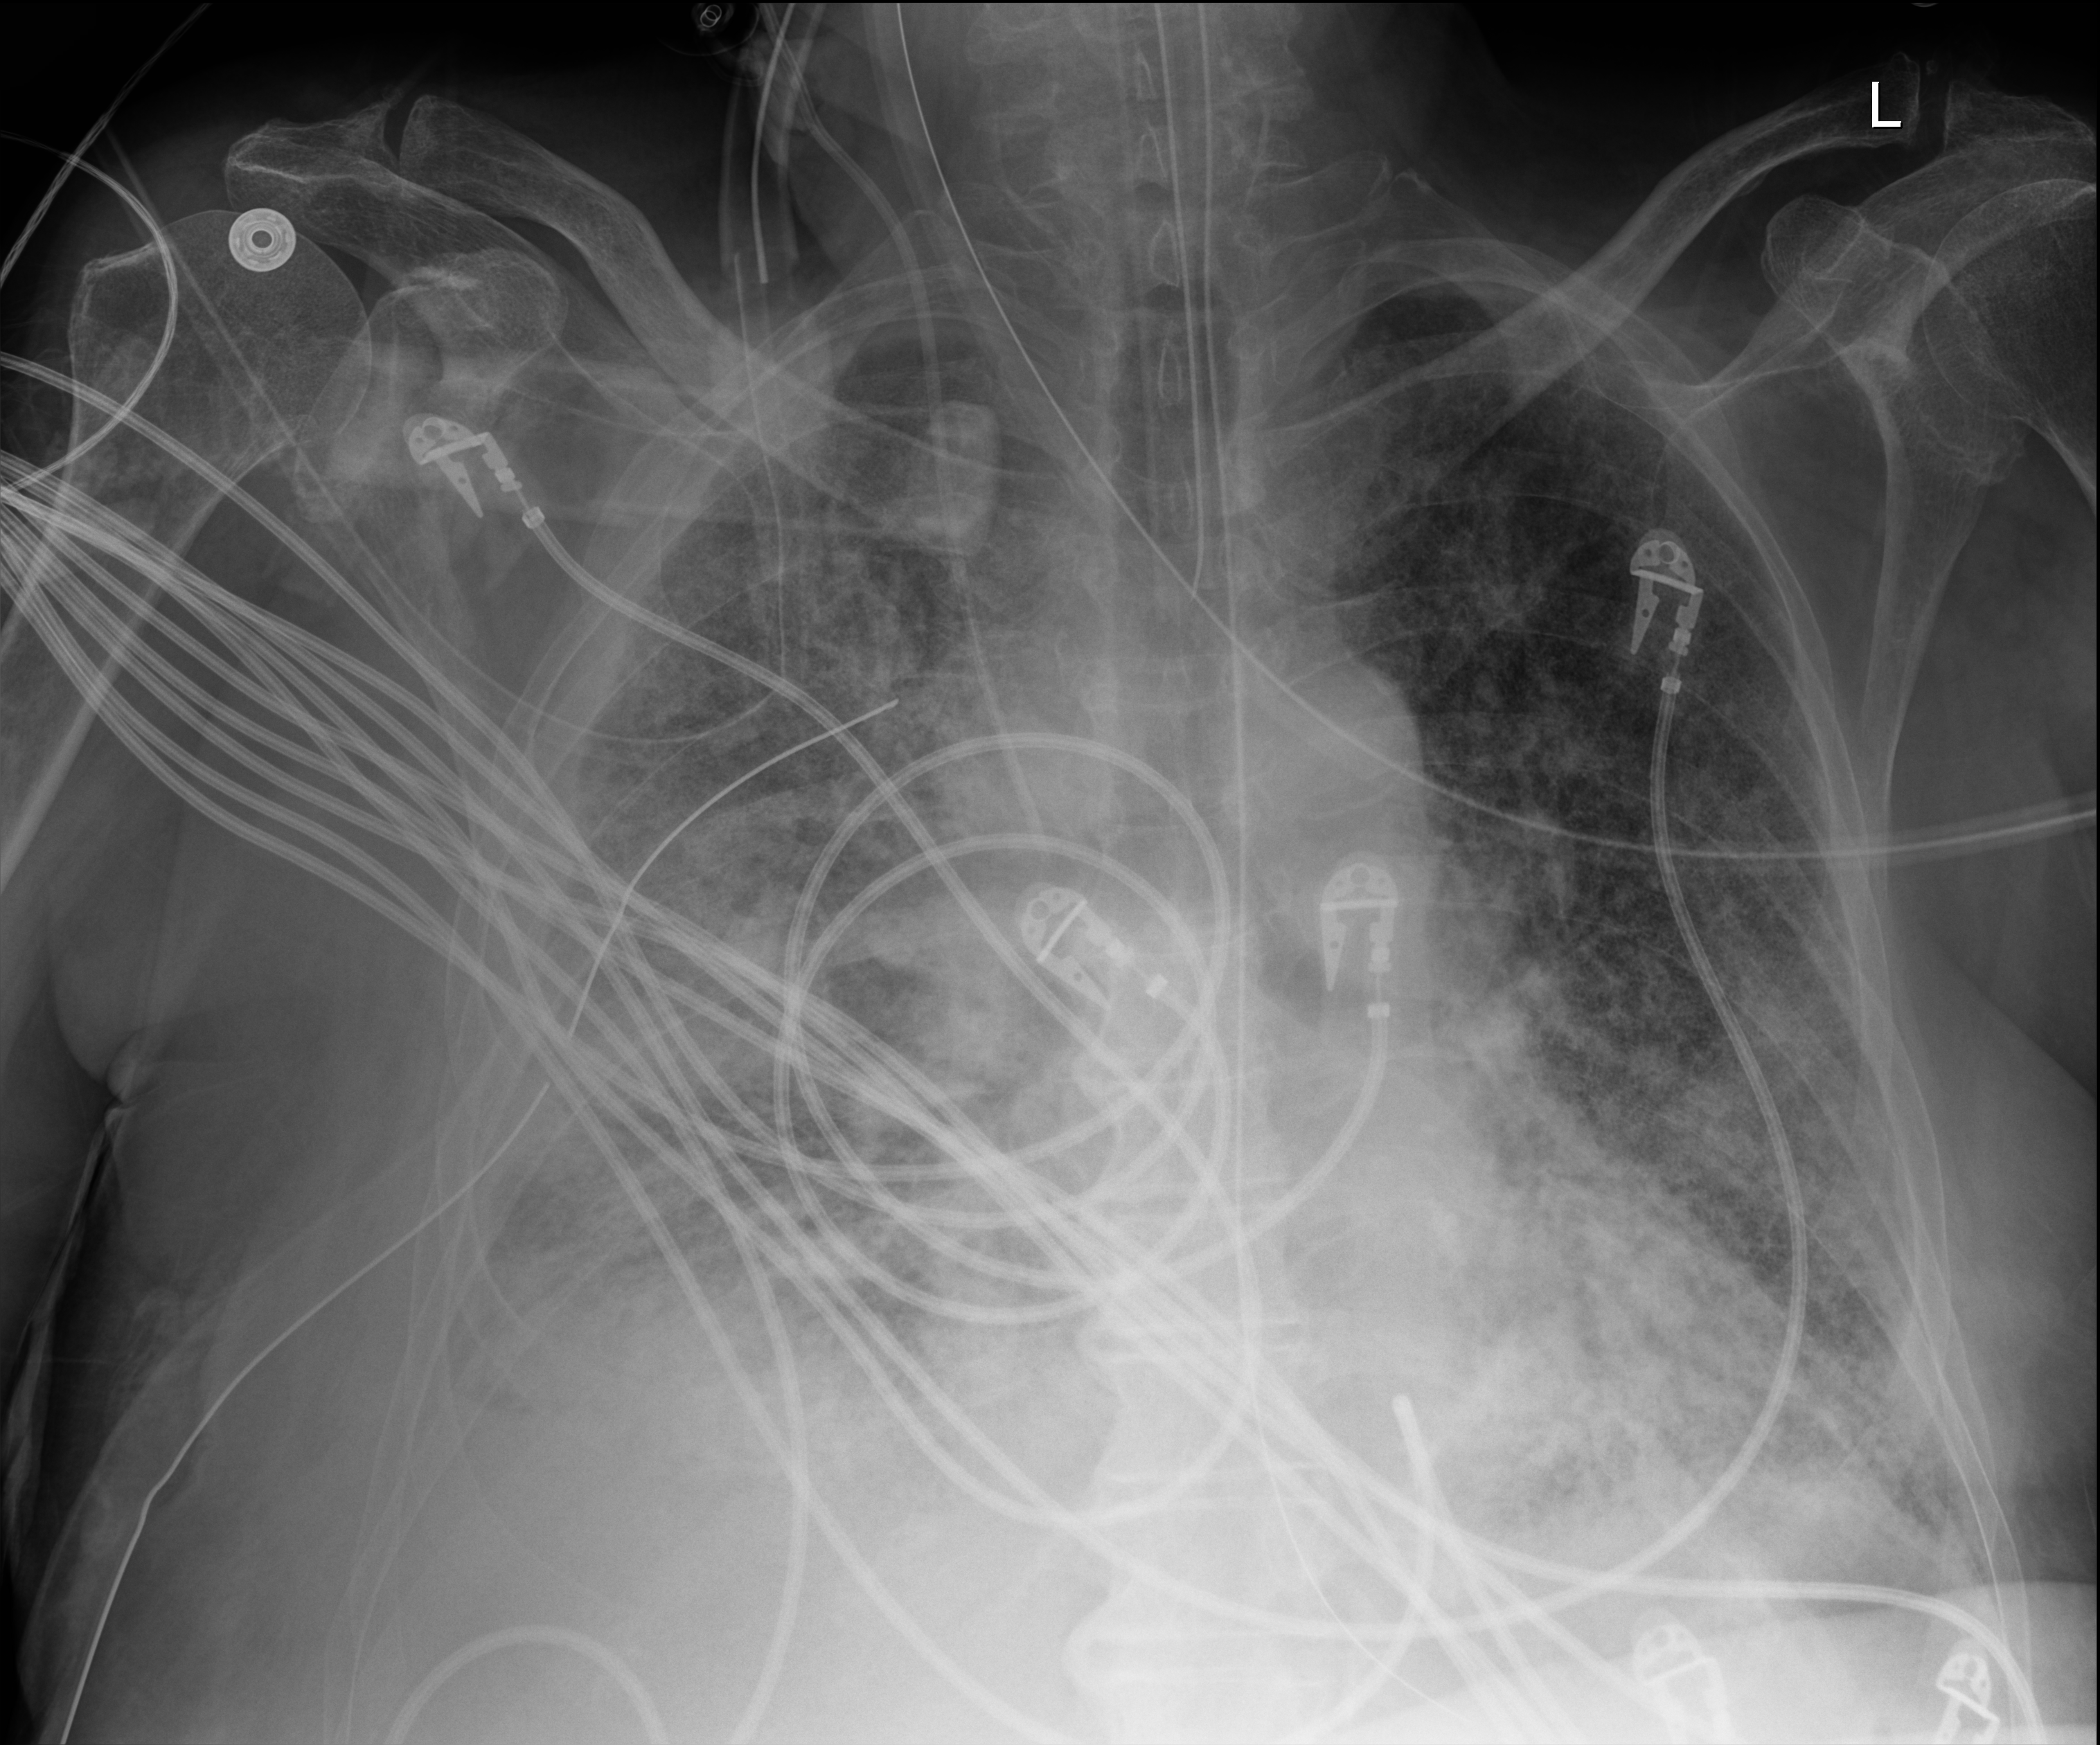
Chest X-ray (portable), anteroposterior (AP) projection. Patient hospitalised with COVID-19; male, aged 75–90 years.
Admission-level facts for this patient (not findings on this image; timing relative to this image not recorded):
- mechanically ventilated during this hospital stay: yes
- admitted to intensive care during this hospital stay: yes